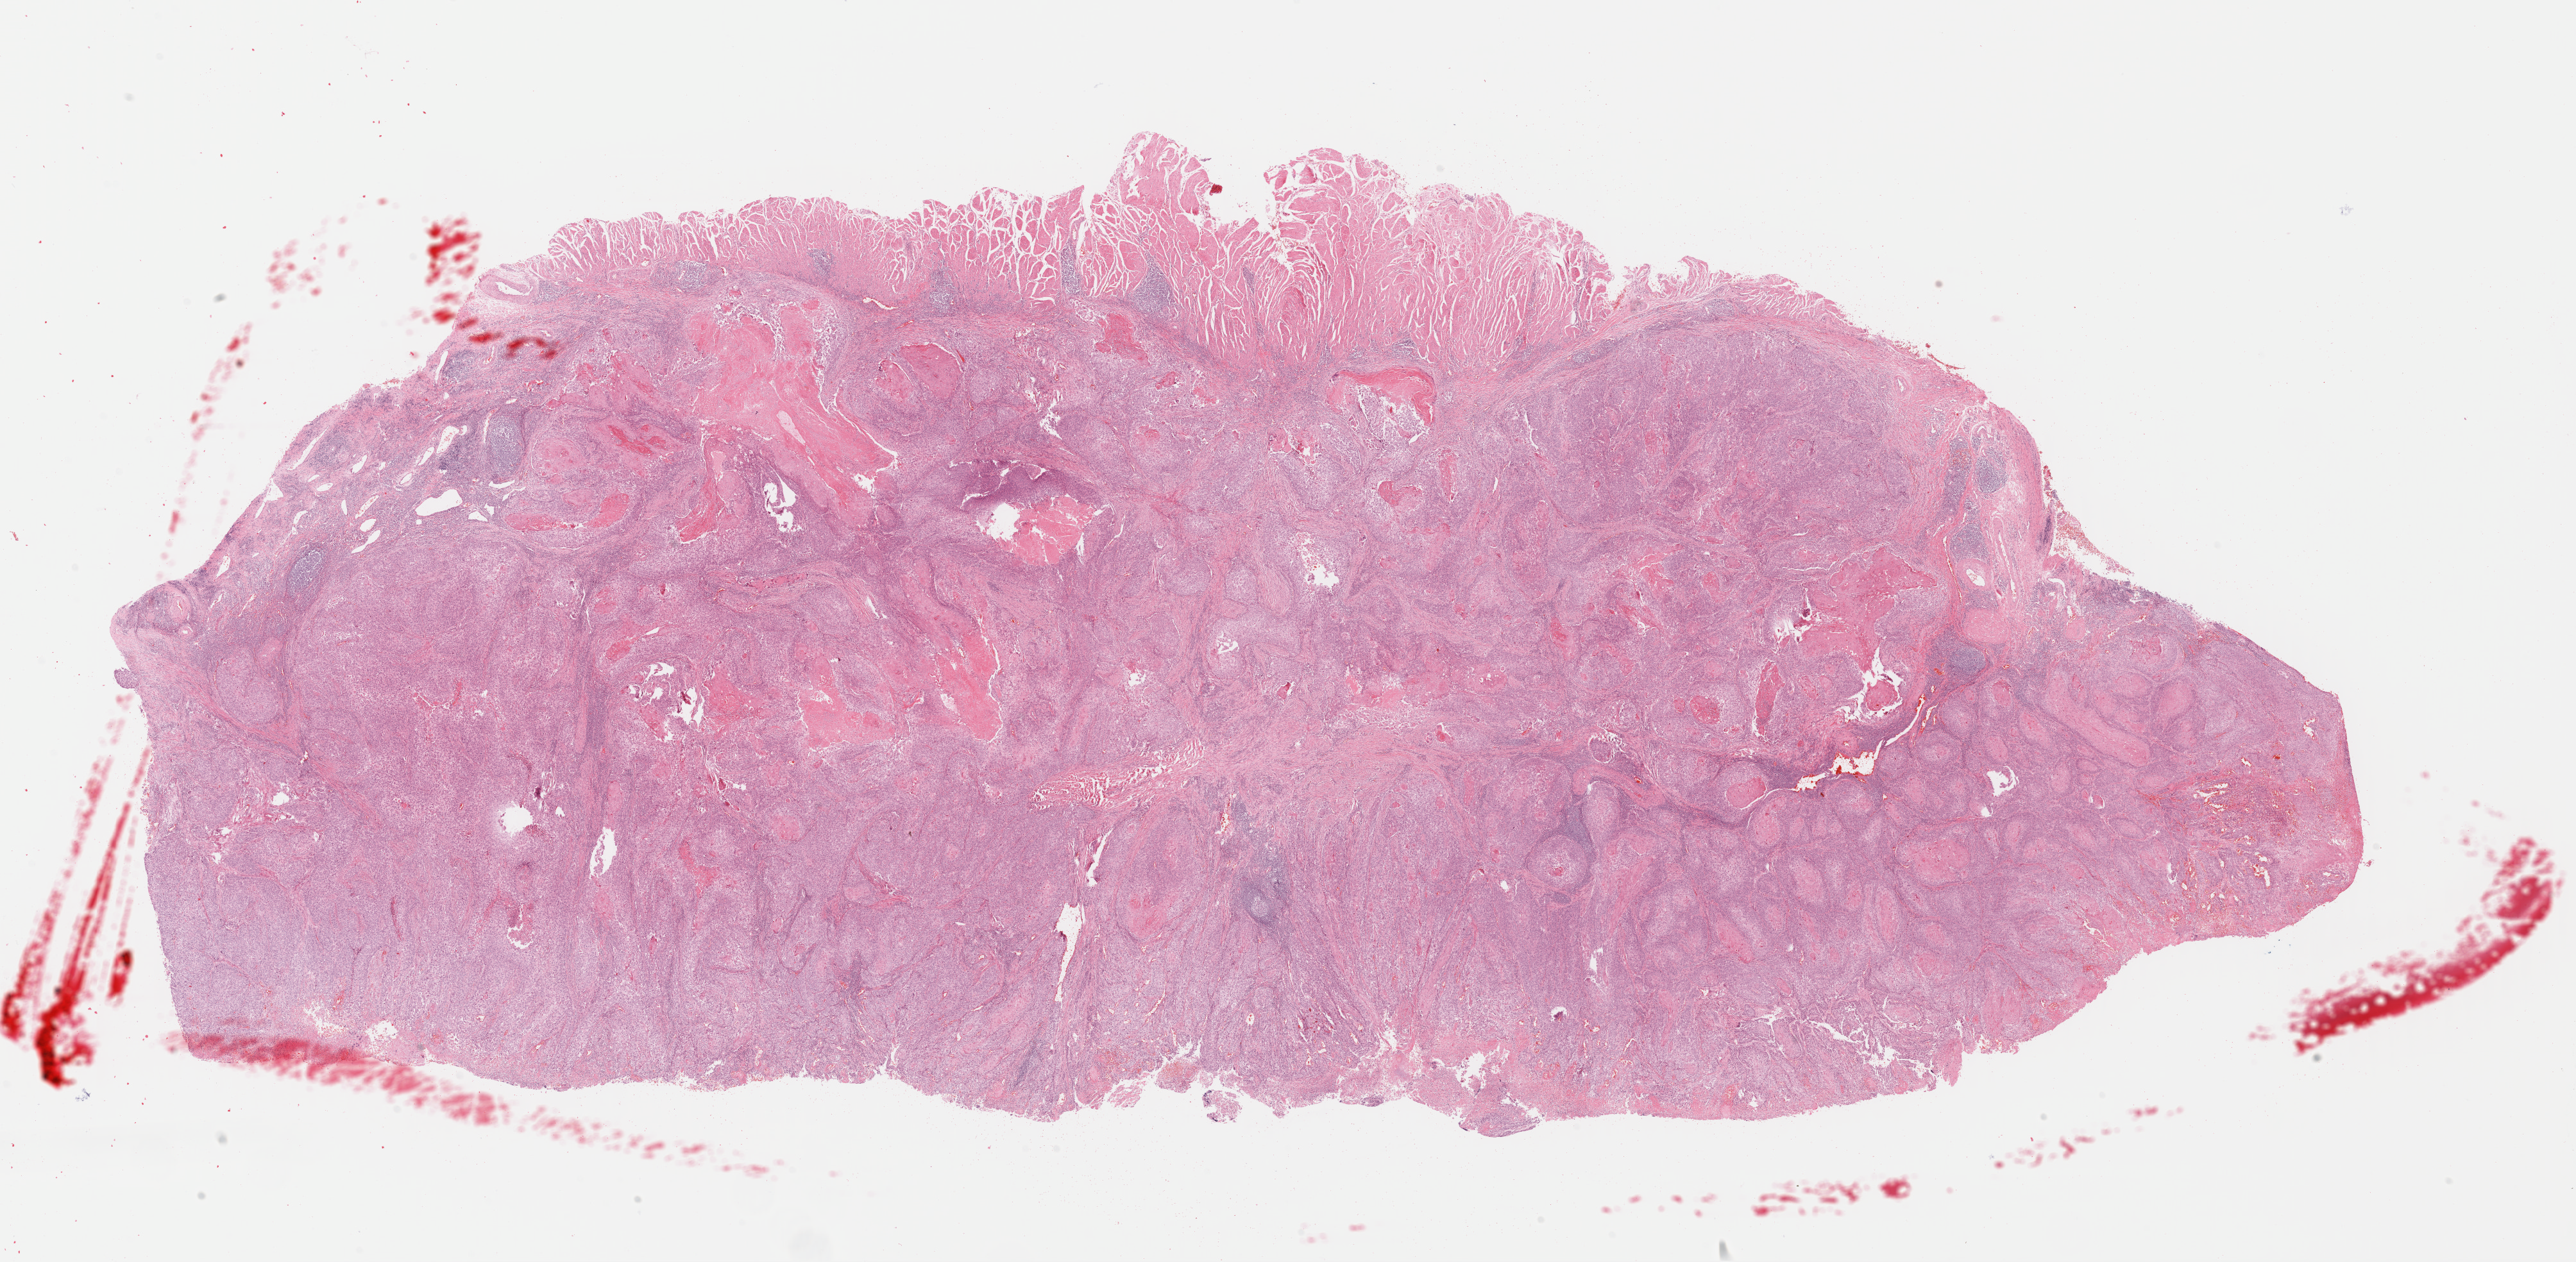
Digitized H&E-stained tissue section (whole slide) — whole scanned area (about 31.6 x 15.5 mm, slide scanned at 40x) shown as a low-resolution overview. Formalin-fixed paraffin-embedded (FFPE) diagnostic section. Sample: primary tumour, esophagus. Patient: male, age at initial diagnosis 63 years. Histologic grade: G2 (moderately differentiated).
- AJCC pathologic stage: IIB
- diagnosis: Squamous cell carcinoma, NOS (upper third of esophagus)
- lymph nodes positive (case pathology): 1 of 1 examined
- TNM: T1 N1 M0